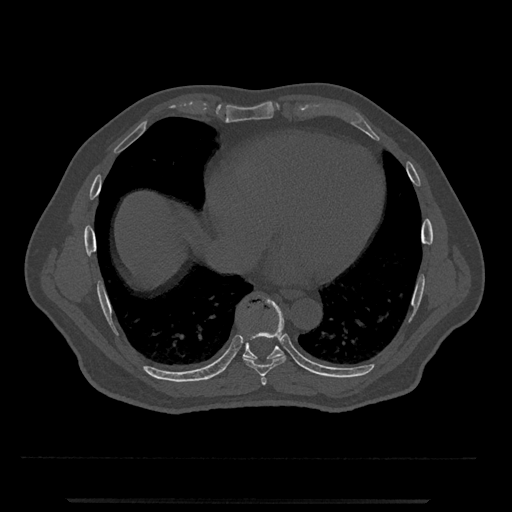
CT including the spine, one axial slice; position 605 of 797 along the scan axis; bone window (W 1800 / L 400 HU); 0.5 mm slice thickness; 512 × 512 image matrix, field of view 419 × 419 mm. Male patient, age 63 years. From the clinical record (not read from this slice): primary cancer: prostate.
Outlined on this slice (semi-automatically segmented with operator editing):
- T7 vertebra: bounding box <261,374,267,385> (left, top, right, bottom; pixels)
- T8 vertebra: <243,298,286,376>
- T9 vertebra: <221,308,283,373>